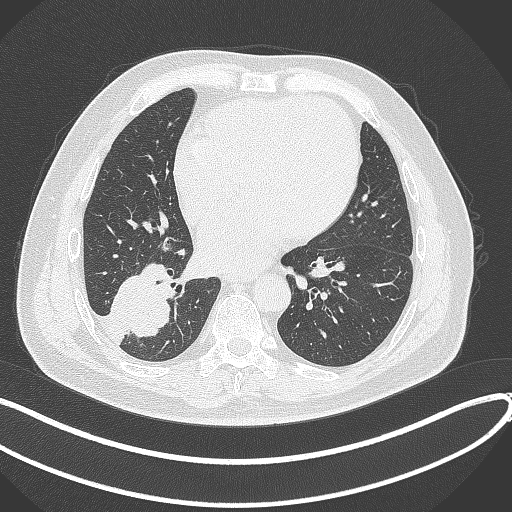
Chest CT, one axial slice. Slice 144 of 360 in the series (ordered by position). 120 kVp. Lung window (W 1500 / L -600 HU). 512 × 512 image matrix, field of view 400 × 400 mm. Patient: male, 59 years.
Annotated regions visible in this slice (rectangle marked by the reading radiologist):
- lung tumour (recorded histology: adenocarcinoma): bounding box (x1, y1, x2, y2) in pixels: (109, 254, 179, 340)